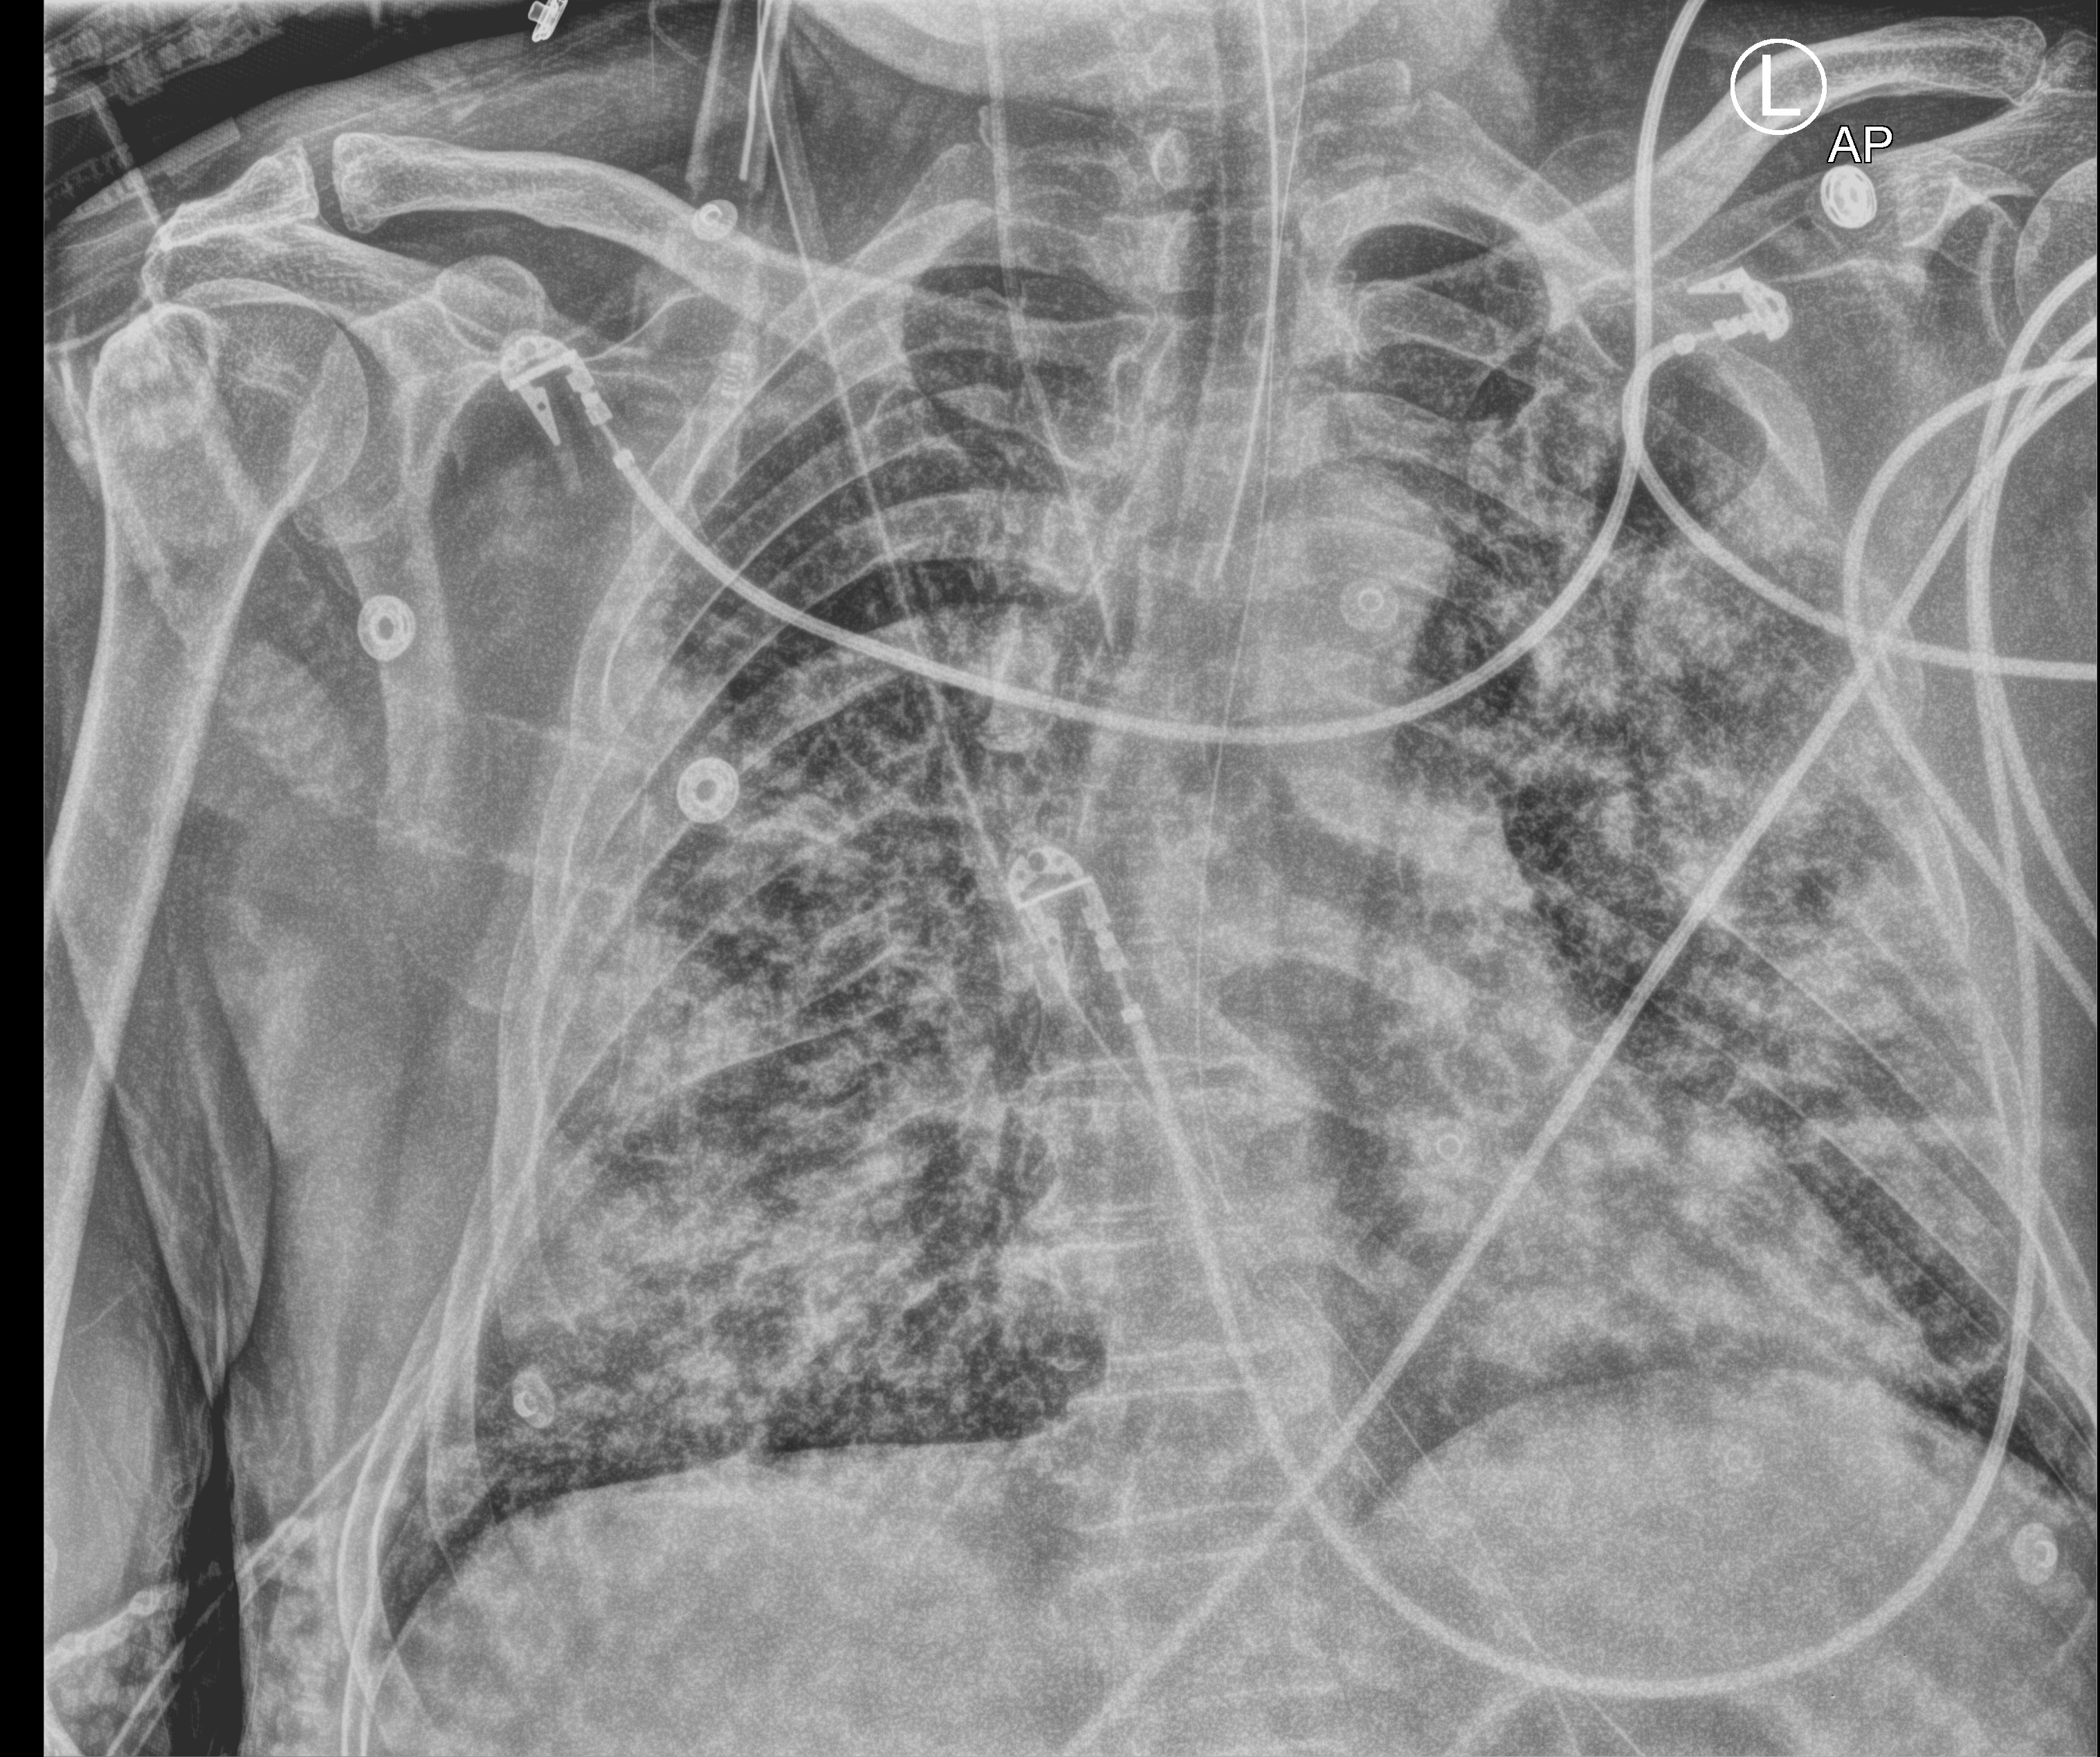
Chest X-ray (portable); anteroposterior (AP) projection. Patient hospitalised with COVID-19; male, aged 60–74 years.
From the hospital-stay record, not from the radiograph (when in the stay this image was taken is not recorded): mechanically ventilated during this hospital stay: yes.